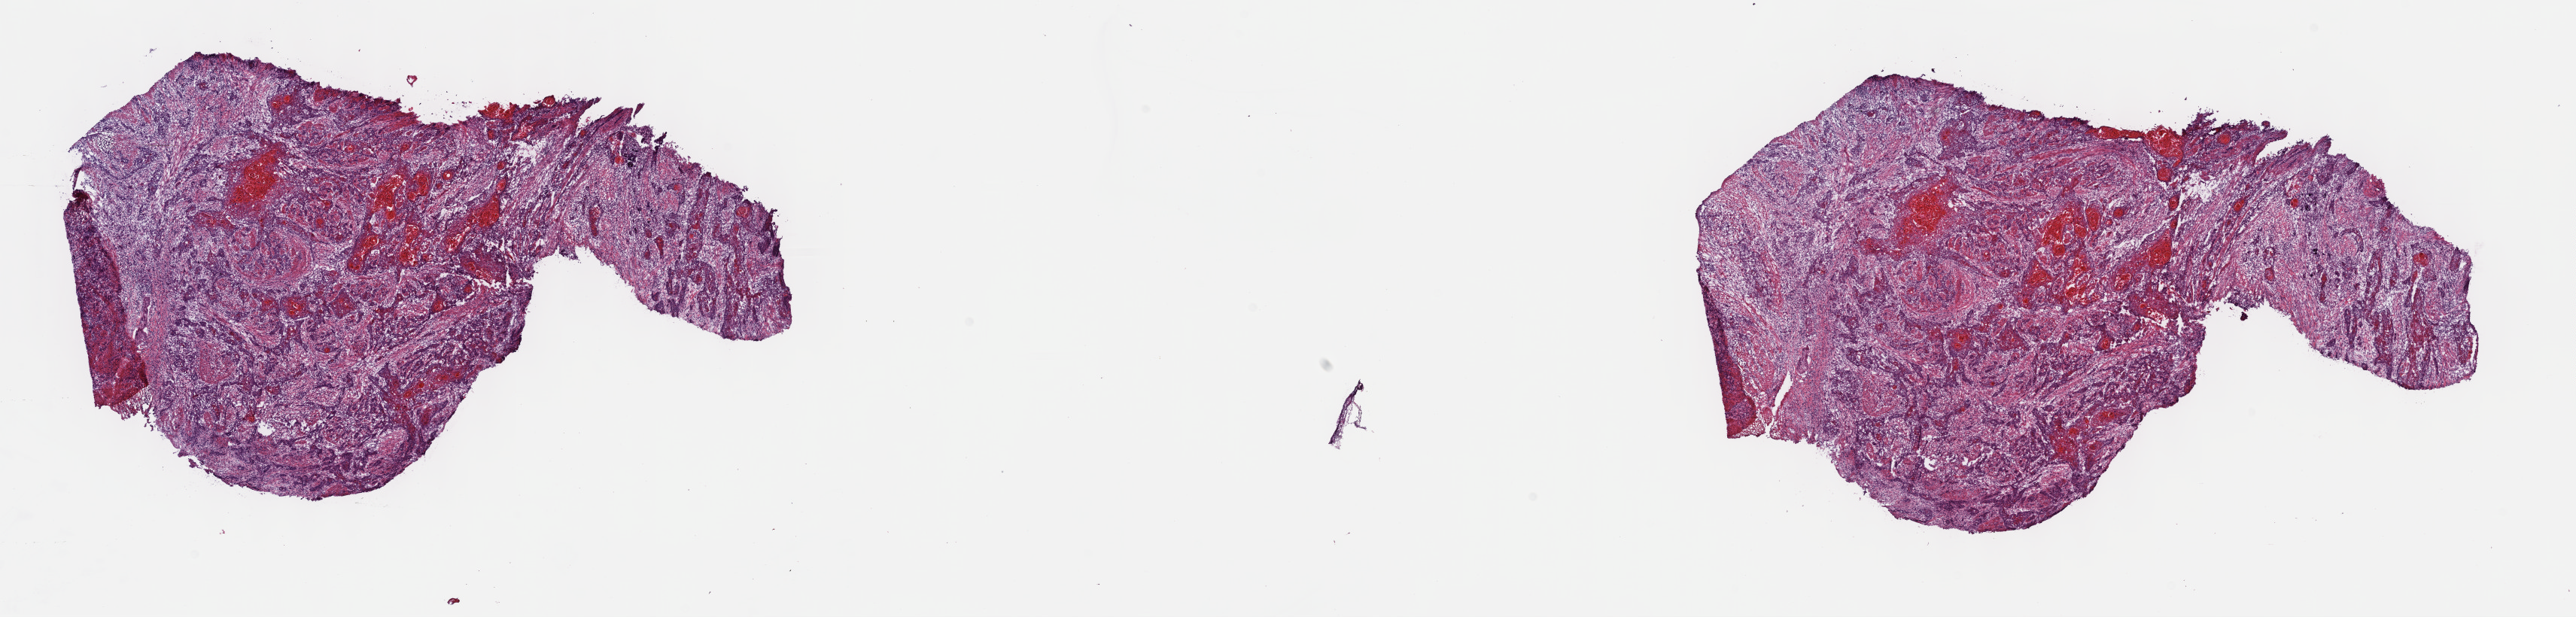
Digitized H&E tissue section (whole slide), shown as a low-resolution overview of the whole scanned area (about 27.7 x 6.6 mm, from a 40x scan); frozen section from the top of the tissue portion; esophagus, primary tumour sample. Male, age 70 years at initial diagnosis. Histologic grade: G1 (well differentiated). Composition of this section per pathologist review: tumour cells 95%, tumour nuclei 60%, normal cells 0%, stromal cells 0%, necrosis 5%. Inflammatory infiltration, as recorded: lymphocyte infiltration 0%, monocyte infiltration 0%, neutrophil infiltration 0%.
TNM: T4 N0 M0. AJCC pathologic stage: III. Lymph nodes positive (case pathology): 0 of 15 examined. Pathologic diagnosis: Squamous cell carcinoma, NOS (middle third of esophagus).